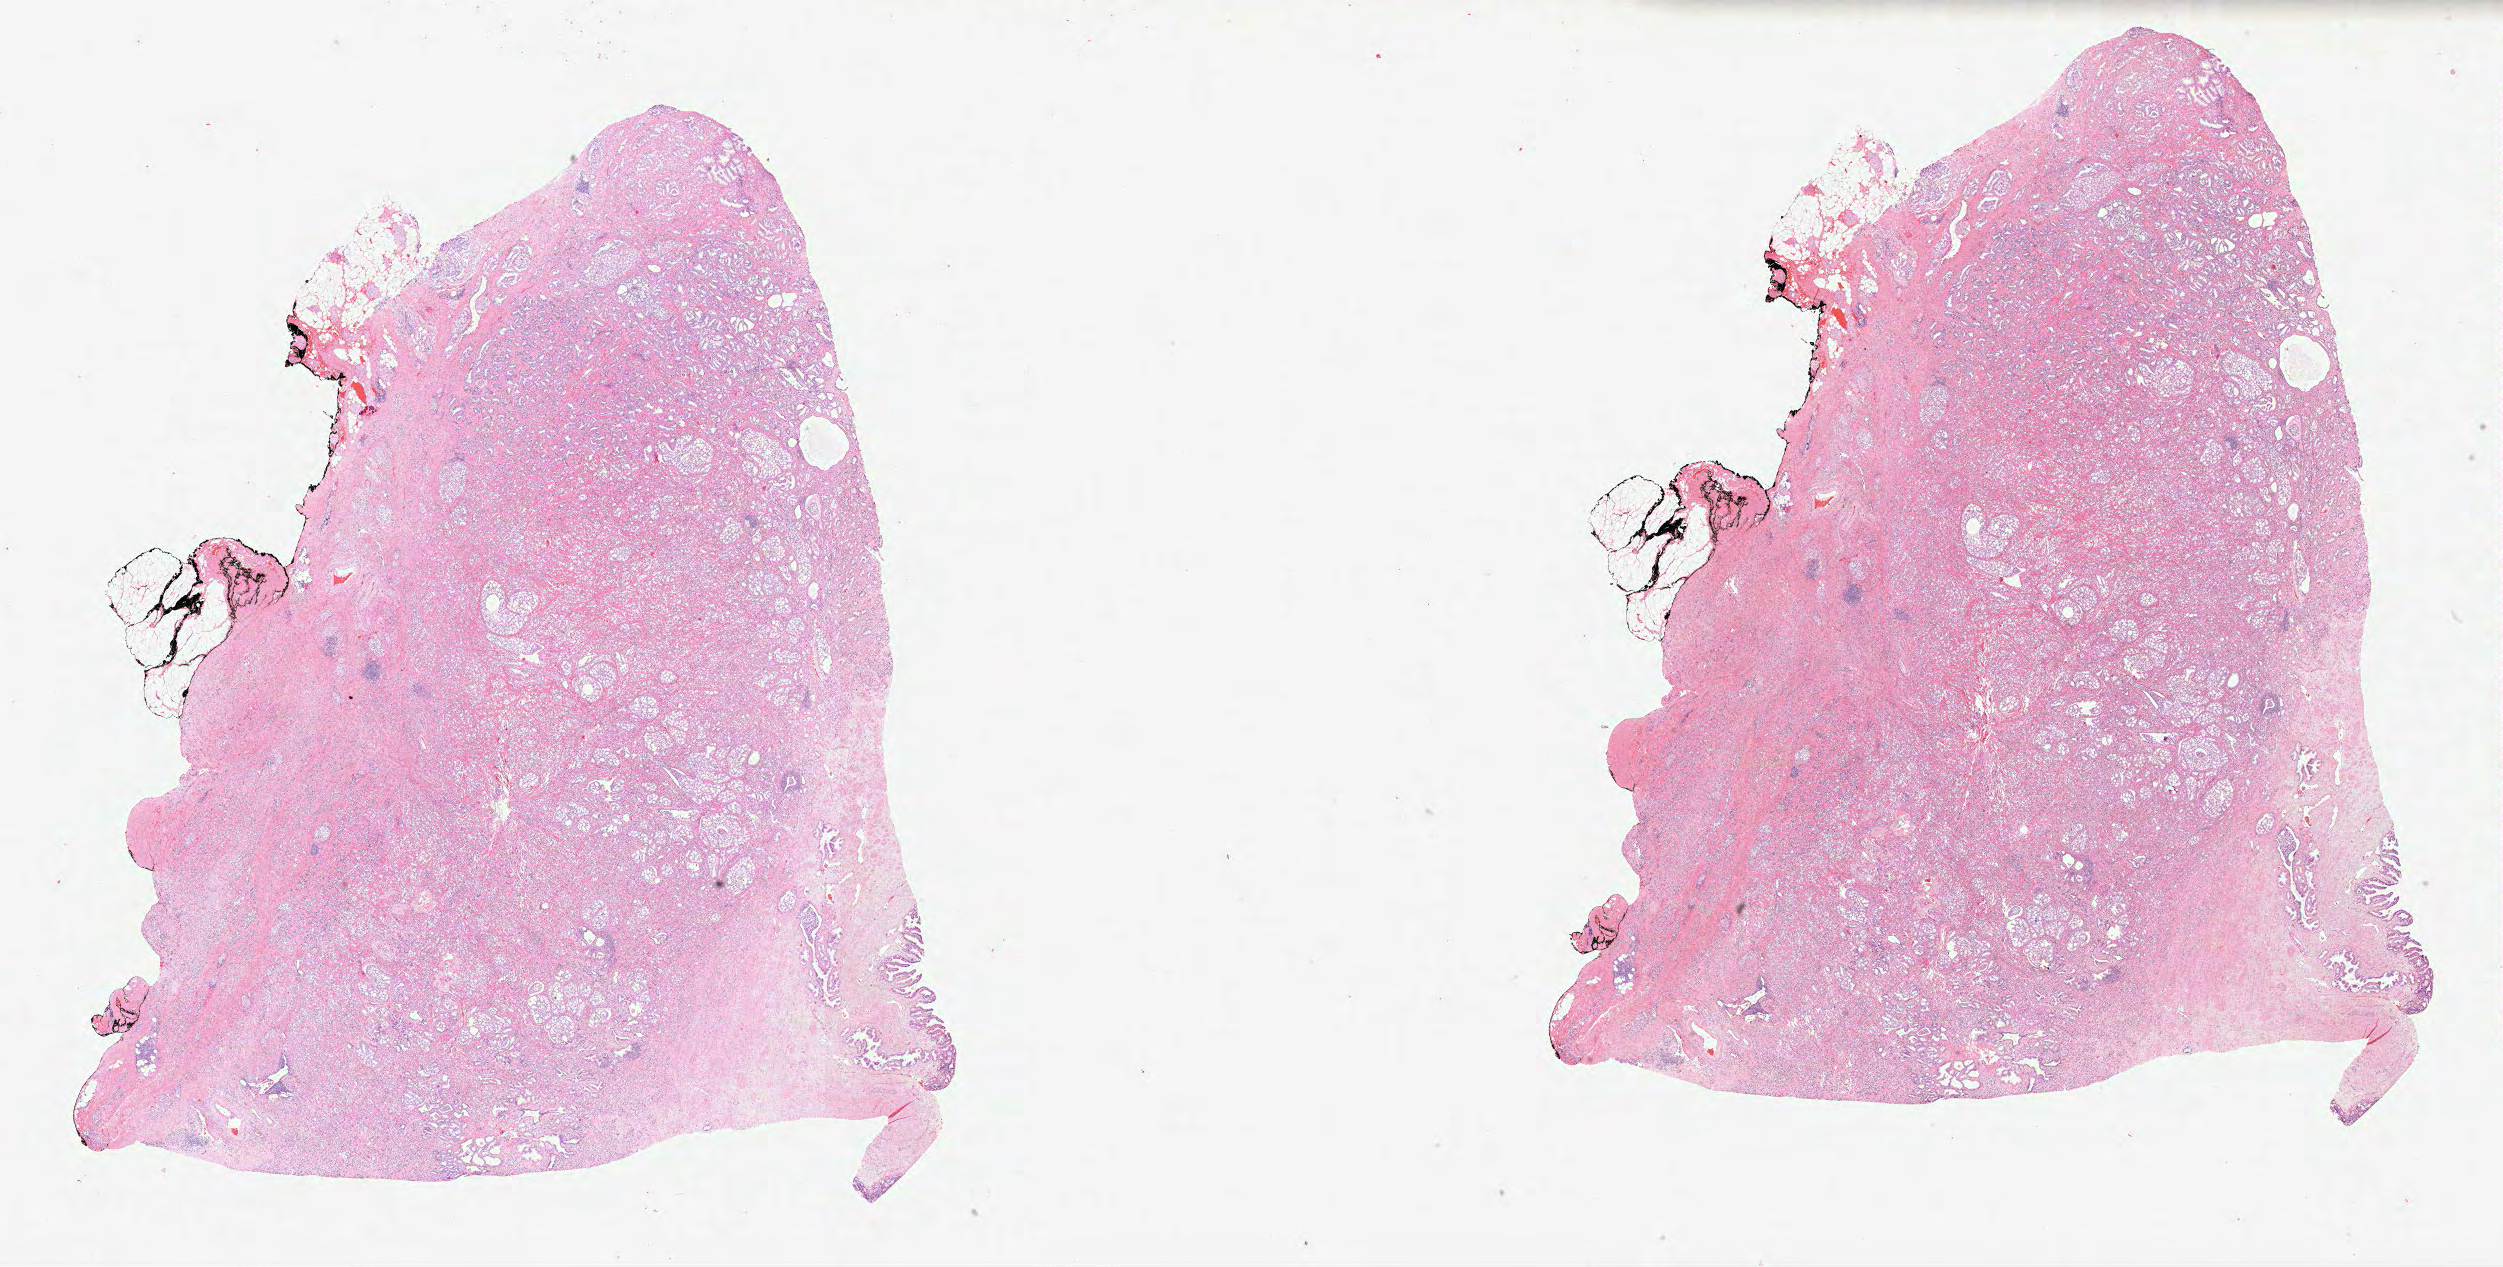
Whole-slide histology image, H&E, a low-resolution overview of the entire scanned area, about 40.4 x 20.4 mm (acquisition: 40x scan). Formalin-fixed paraffin-embedded (FFPE) diagnostic section. Prostate, primary tumour sample. Patient: male, age at initial diagnosis 60 years. Gleason score: 9 (4+5).
Histologic diagnosis: Acinar cell carcinoma (prostate gland). Lymph nodes positive (case pathology): 0 of 5 examined.